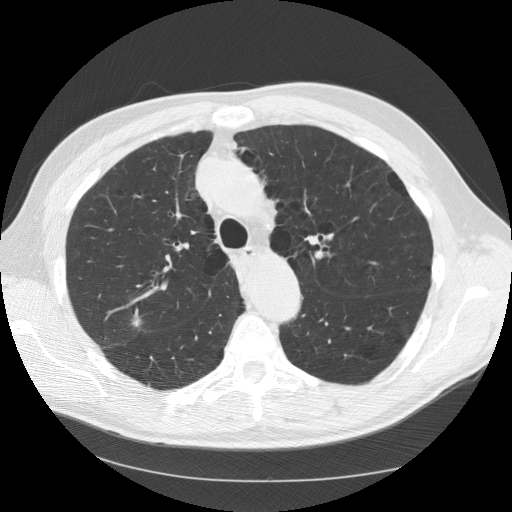
Low-dose screening chest CT, one axial slice; position 91 of 133 along the scan axis; reconstruction kernel STANDARD; 120 kVp; lung window (W 1500 / L -600 HU); 512 × 512 image matrix, field of view 377 × 377 mm.
Structures marked on this image (outlined manually by an expert reader):
- lesion 1 (tumor, upper lobe of right lung): box from (x=131, y=309) to (x=142, y=327) px